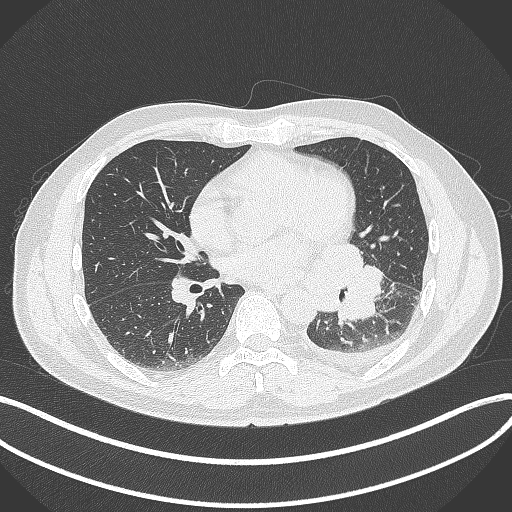
Chest CT, one axial slice. Slice 166 of 342 in the series (ordered by position). Lung window (W 1500 / L -600 HU). 1 mm slice thickness. 512 × 512 image matrix. Male patient, age 58 years. Case-level facts recorded for this patient, not image findings: clinical TNM (as recorded): T3 N1 M1b.
Outlined on this slice (bounding box drawn by a radiologist):
- lung tumour (recorded histology: small cell carcinoma): bounding box (x1, y1, x2, y2) in pixels: (315, 233, 384, 327)